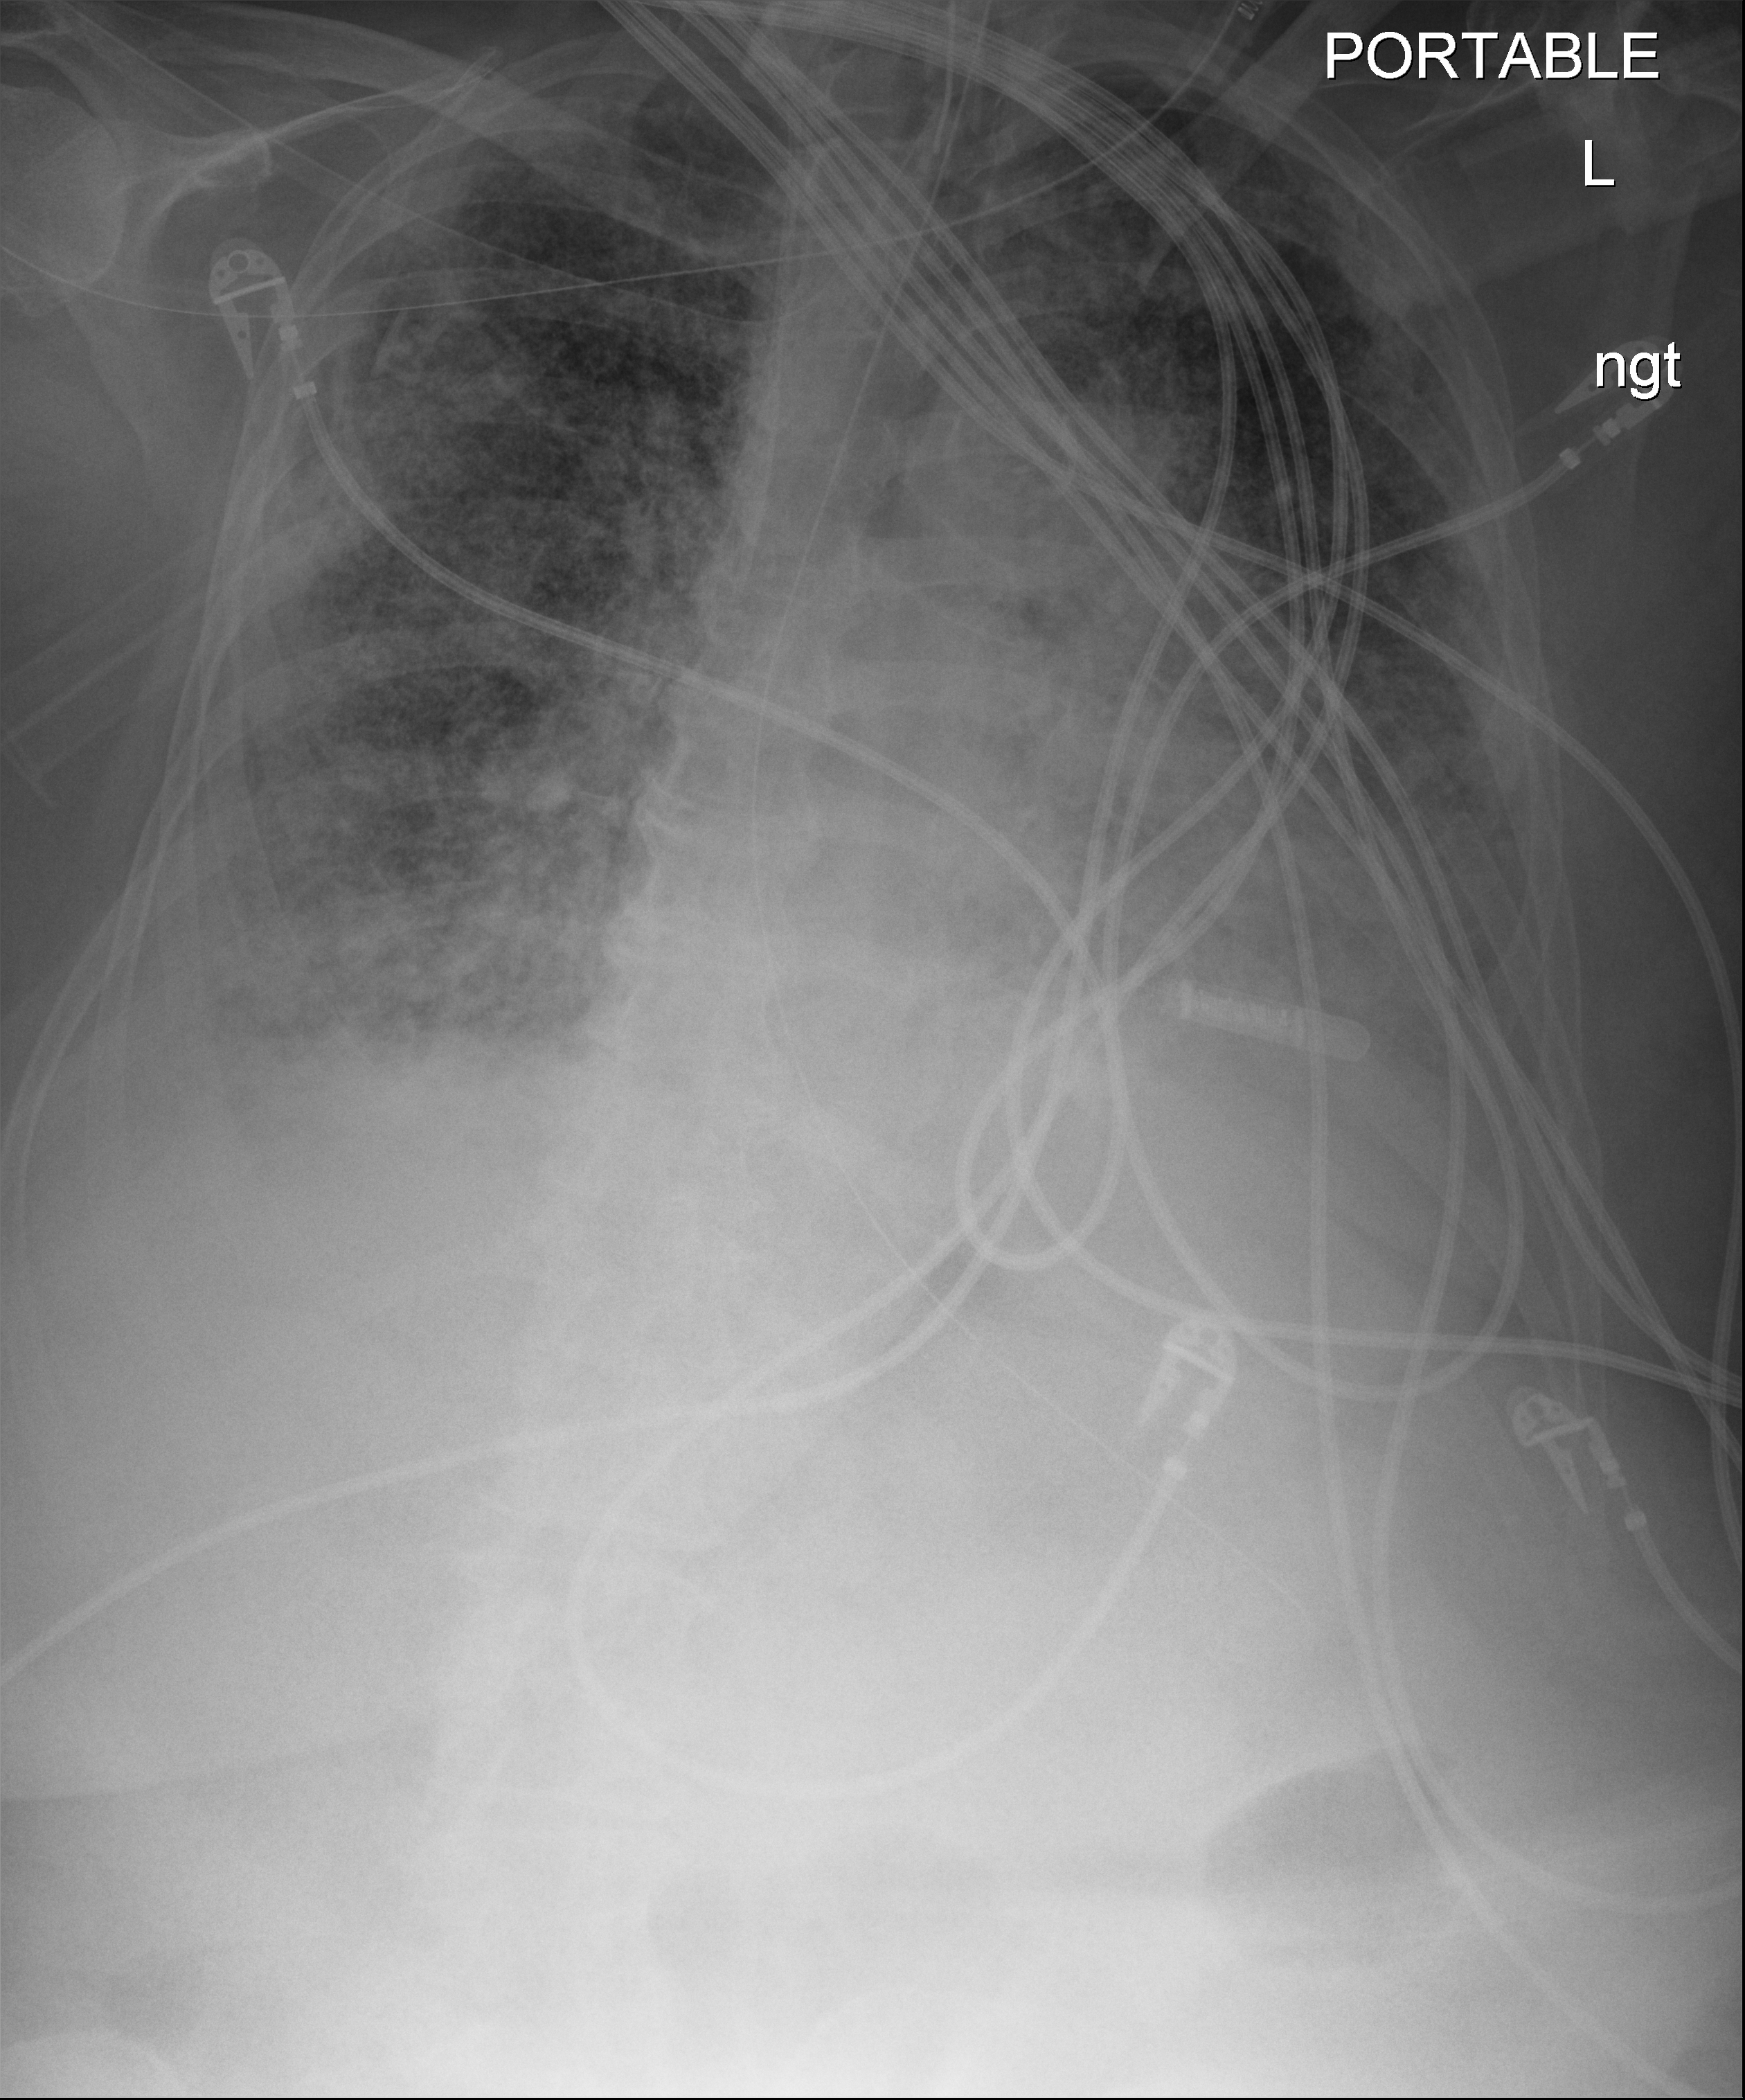
Portable chest radiograph, anteroposterior (AP) projection. Patient hospitalised with COVID-19; female, aged 60–74 years.
From the hospital-stay record, not from the radiograph (when in the stay this image was taken is not recorded): mechanically ventilated during this hospital stay: yes; chronic kidney disease (admission record): no; length of hospital stay: 28 days.